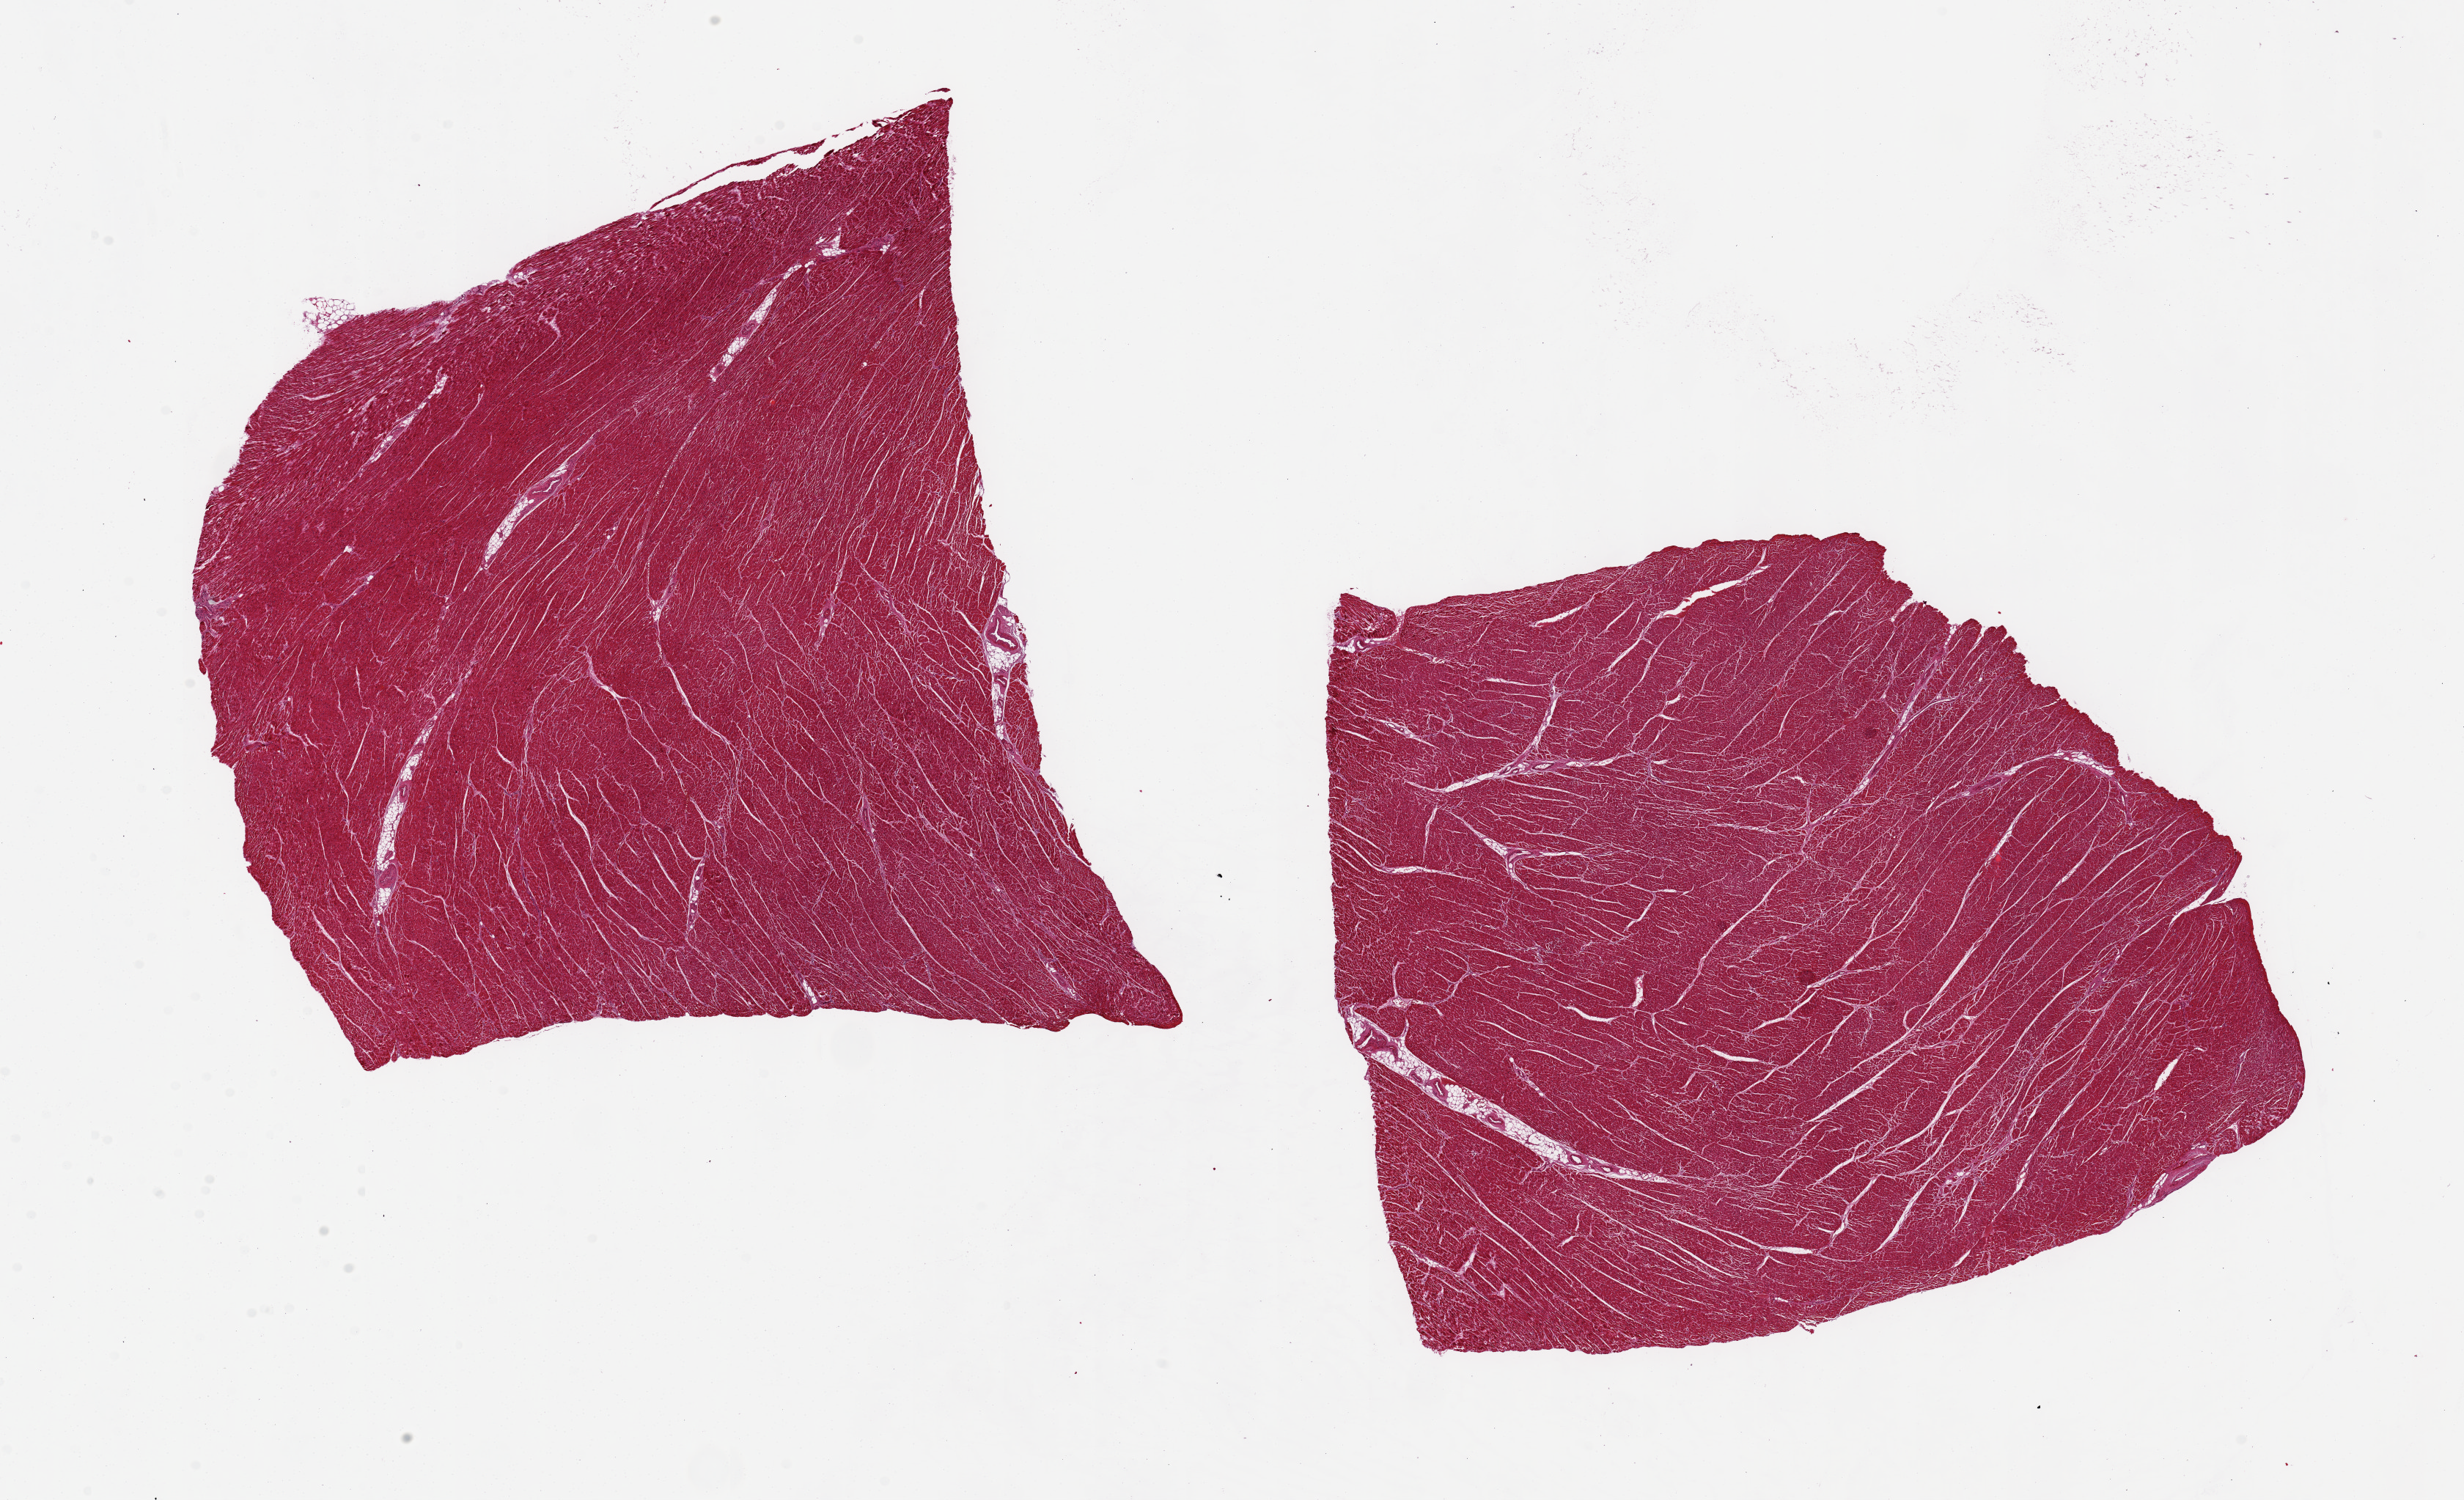
Digitized hematoxylin and eosin (H&E)-stained section, brightfield, low-resolution overview of the scanned area, about 26.6 x 16.2 mm (acquisition: 20x scan), PAXgene-fixed paraffin-embedded (PFPE) section, sampled site (target tissue): heart, donor tissue sample. Donor: male.
Pathologist's review note for this sample: 2 pieces ~10x8mm. Minimal fibrosis/ischemic damage.